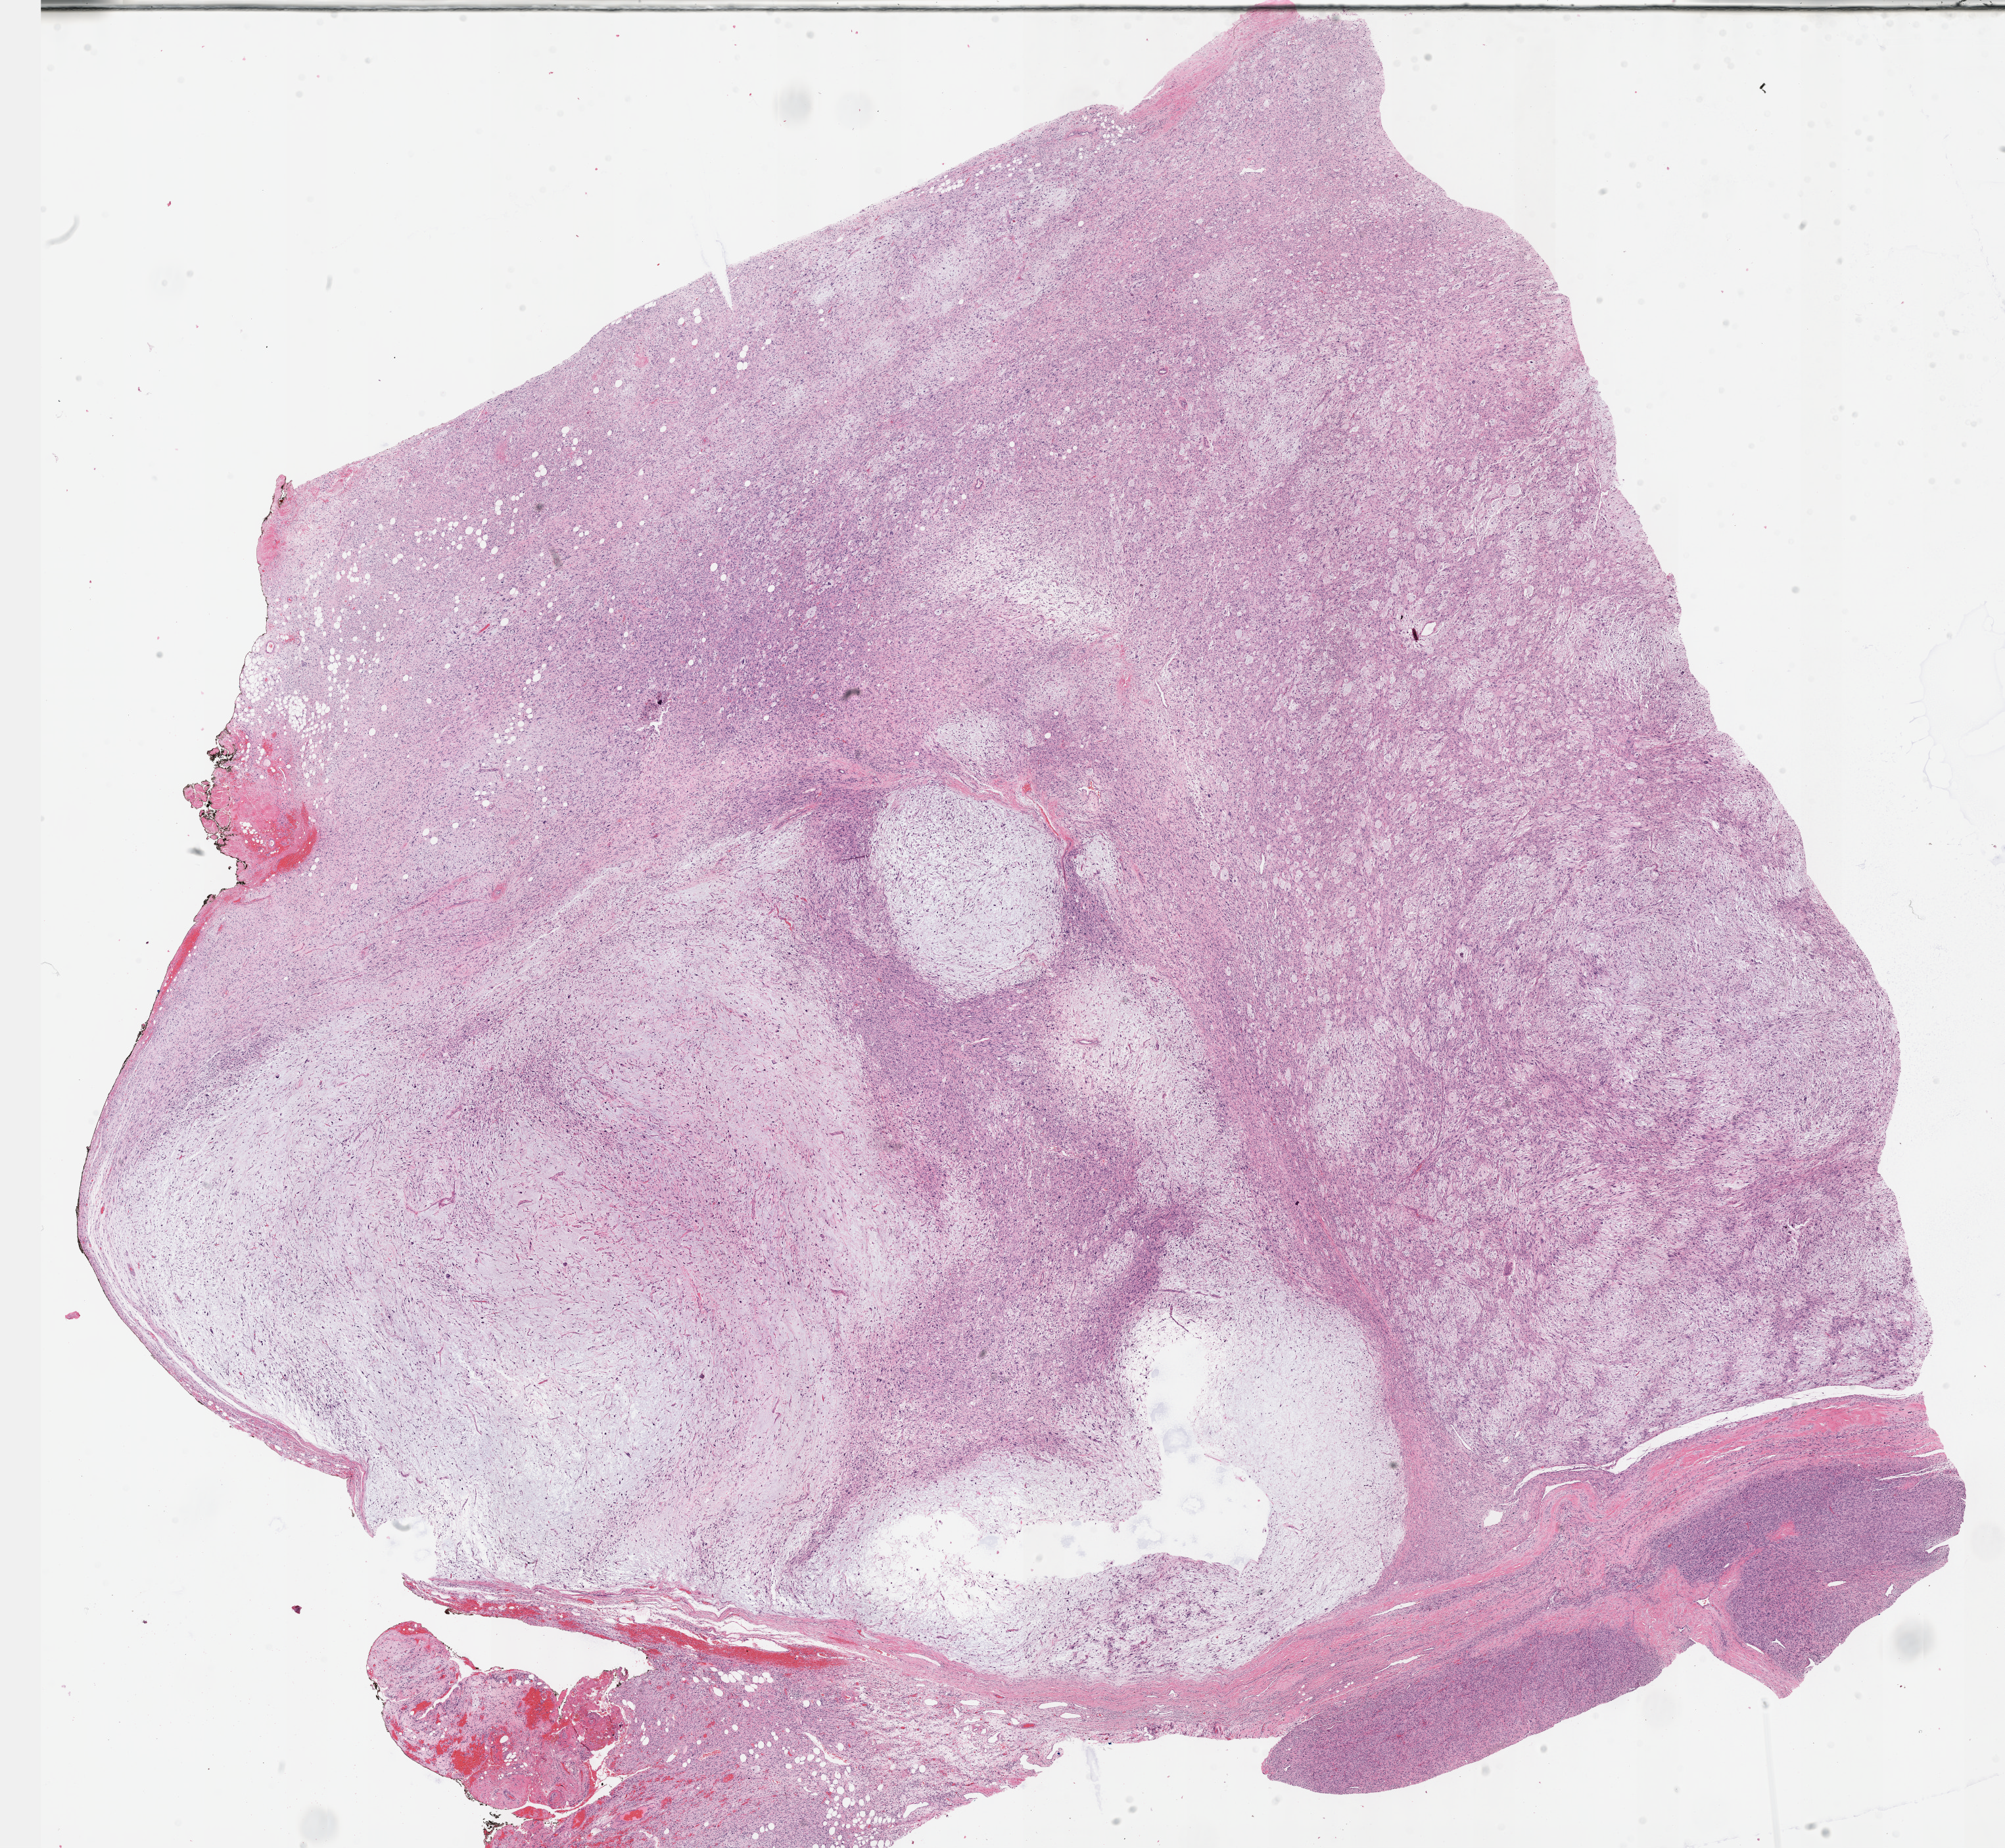
Digitized H&E tissue section (whole slide) — shown as a low-resolution overview of the whole scanned area (about 24.6 x 22.7 mm, acquisition: 40x scan); FFPE section; connective, subcutaneous and other soft tissues, primary tumour sample. Patient: male, age at initial diagnosis 55 years.
• histologic diagnosis: Fibromyxosarcoma (connective, subcutaneous and other soft tissues of lower limb and hip)